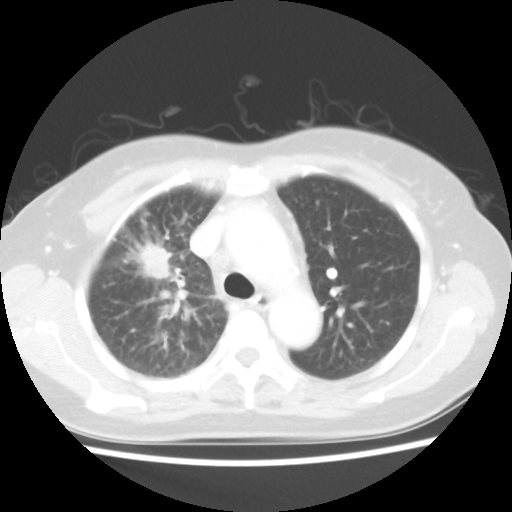
Chest CT, one axial slice. Slice 32 of 48 in the series (ordered by position). 100 kVp. Lung window (W 1500 / L -600 HU). 5 mm slice thickness. 512 × 512 image matrix, field of view 312 × 312 mm. Patient: female, 55 years. From the clinical record (not read from this slice): clinical TNM (as recorded): T1b N3 M1a.
Structures marked on this image (rectangle marked by the reading radiologist):
- lung tumour (recorded histology: adenocarcinoma): bounding box [x1, y1, x2, y2] px = [140, 244, 172, 278]